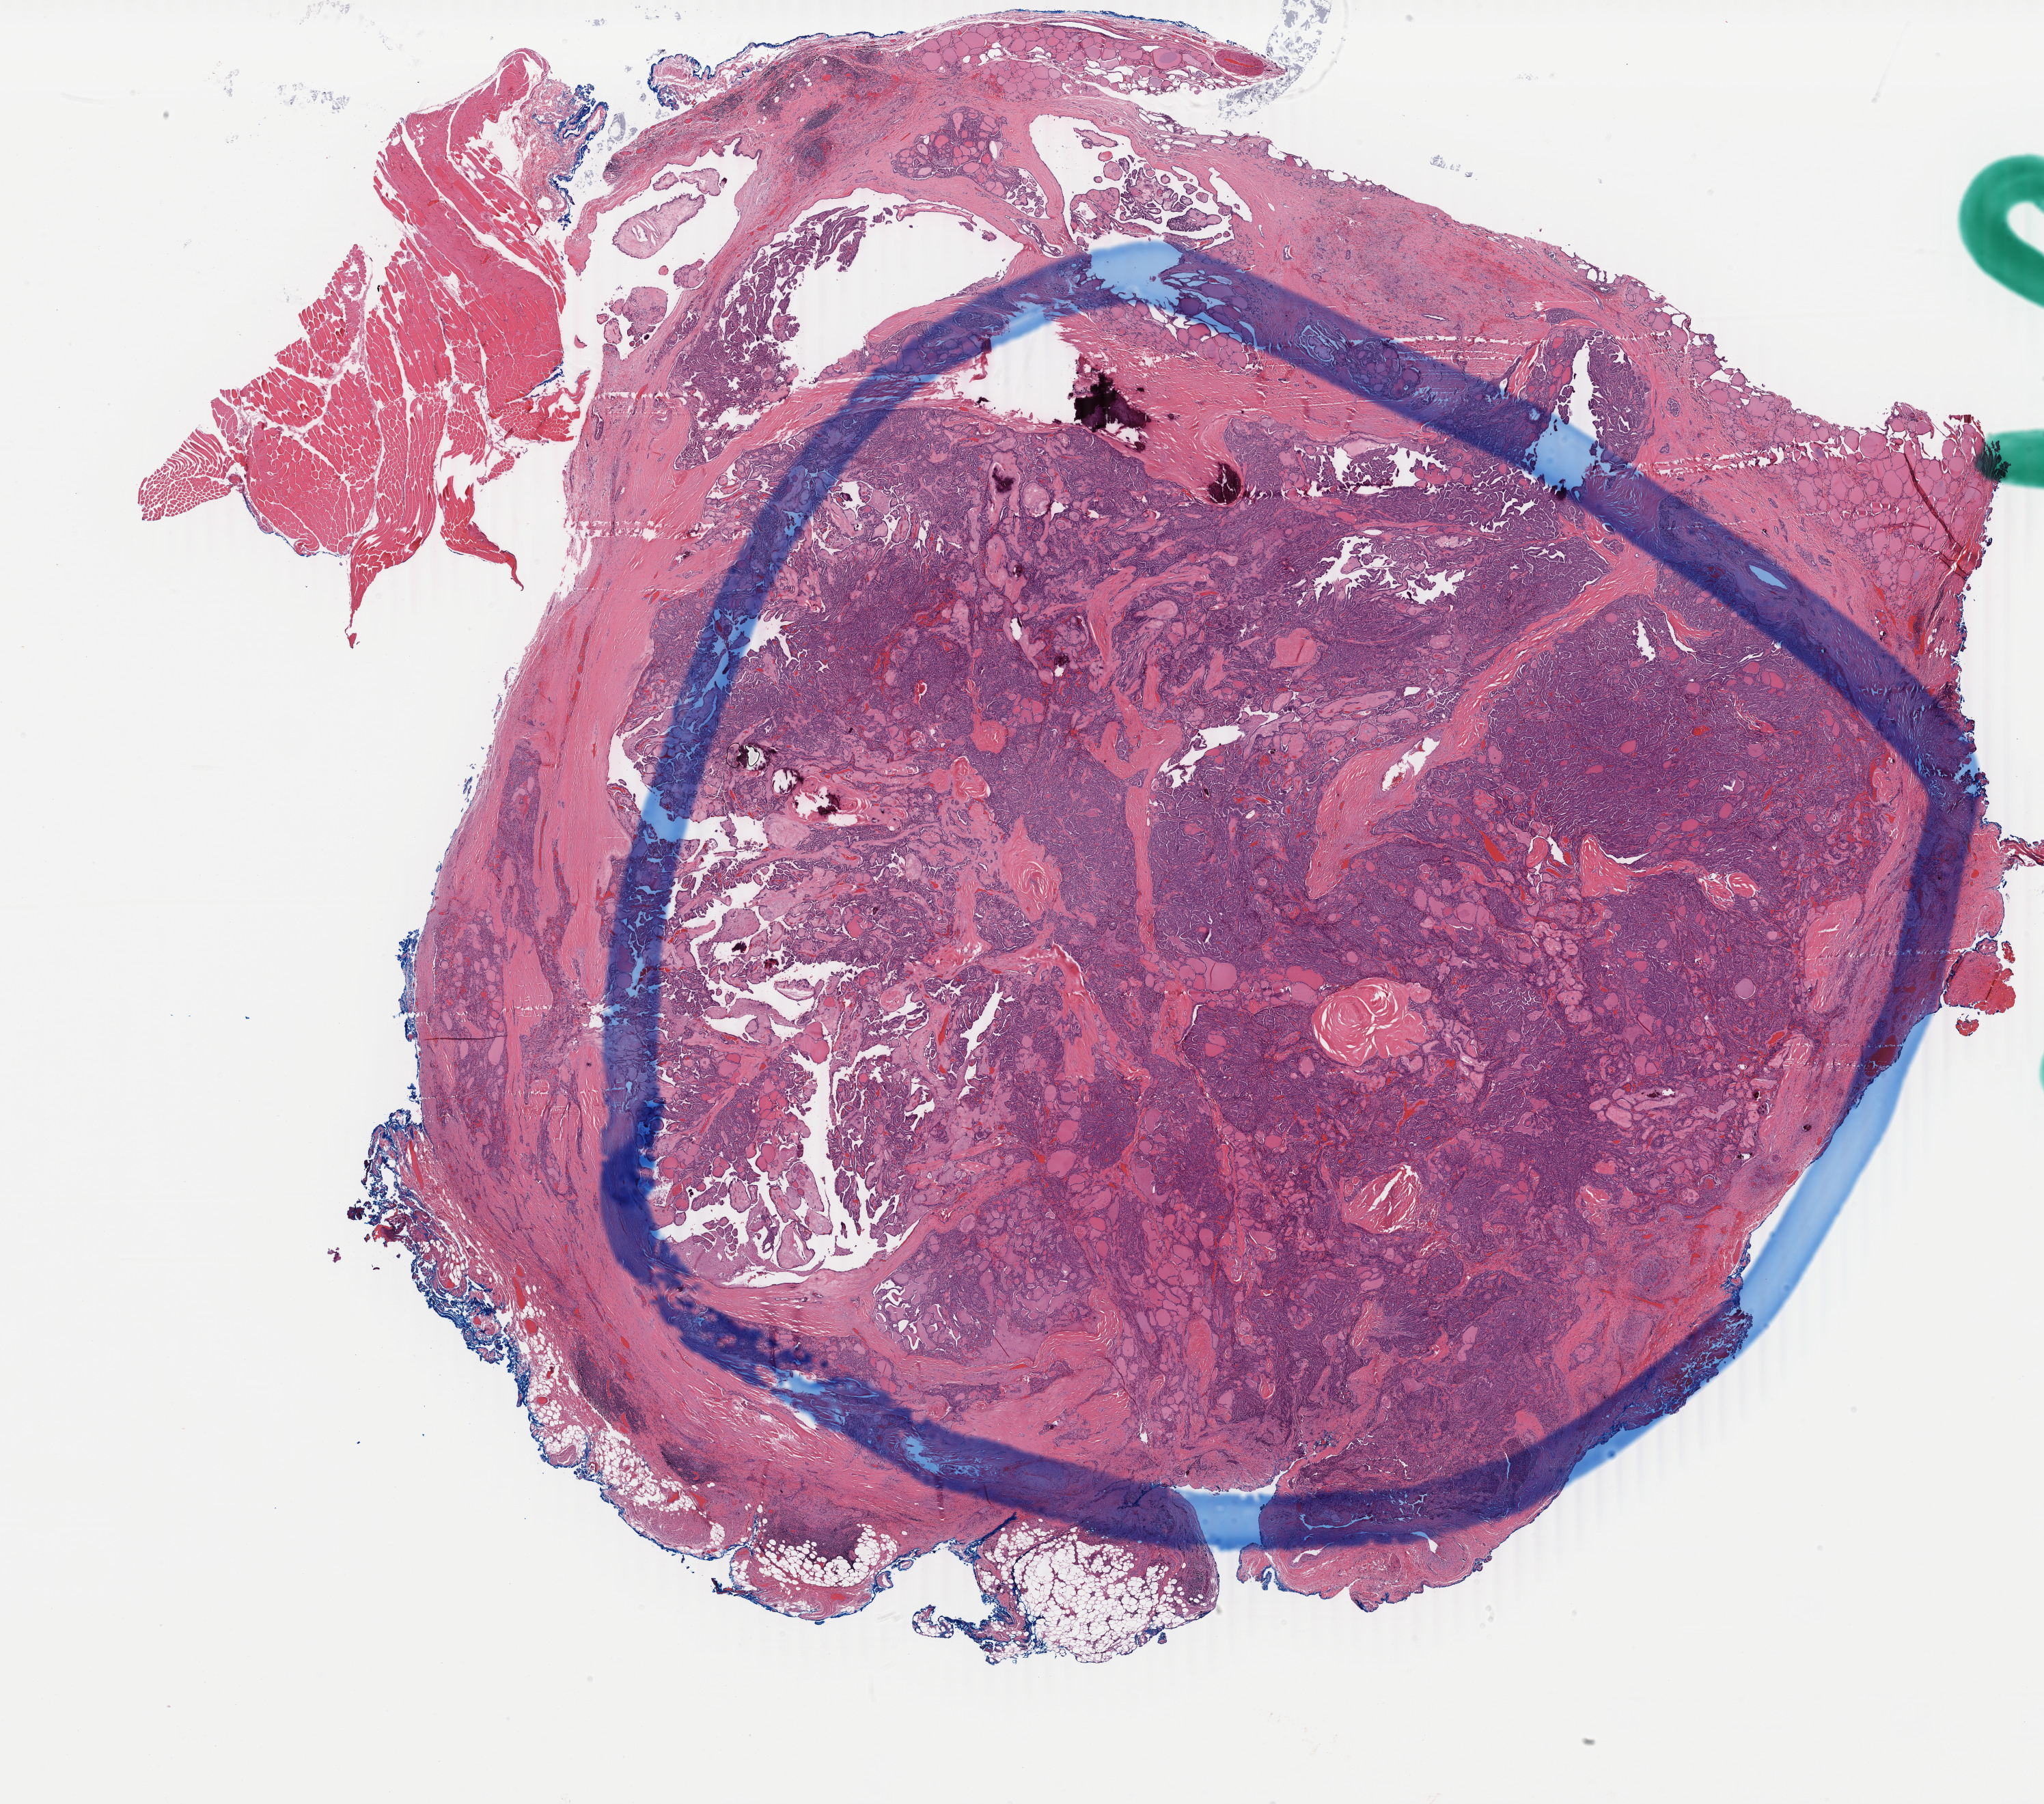
Hematoxylin and eosin (H&E) stained whole-slide image — a low-resolution overview of the entire scanned area, about 23.8 x 21.0 mm (slide scanned at 40x). Formalin-fixed paraffin-embedded (FFPE) diagnostic section. Primary tumour sample from the thyroid. Patient: male, age at initial diagnosis 41 years.
• laterality: left
• lymph nodes positive (case pathology): 8 of 8 examined
• AJCC pathologic stage: I (7th edition)
• histologic diagnosis: Papillary adenocarcinoma, NOS (thyroid gland)